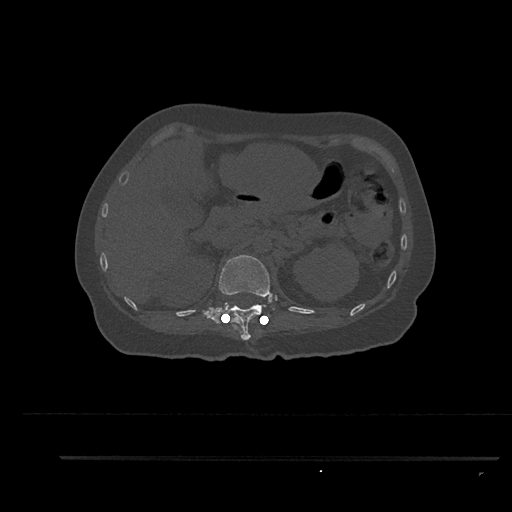
CT including the spine, one axial slice; slice 250 of 797 in the series (ordered by position); reconstruction kernel Br40s/3; 120 kVp; bone window (W 1800 / L 400 HU); 512 × 512 image matrix. Female patient, age 44 years. From the clinical record (not read from this slice): primary cancer: renal; vertebrae with lytic lesions (as recorded): L1.
Outlined on this slice (semi-automatic segmentation, software-assisted and operator-edited):
- T12 vertebra: bounding box (x1, y1, x2, y2) in pixels: (201, 255, 273, 340)